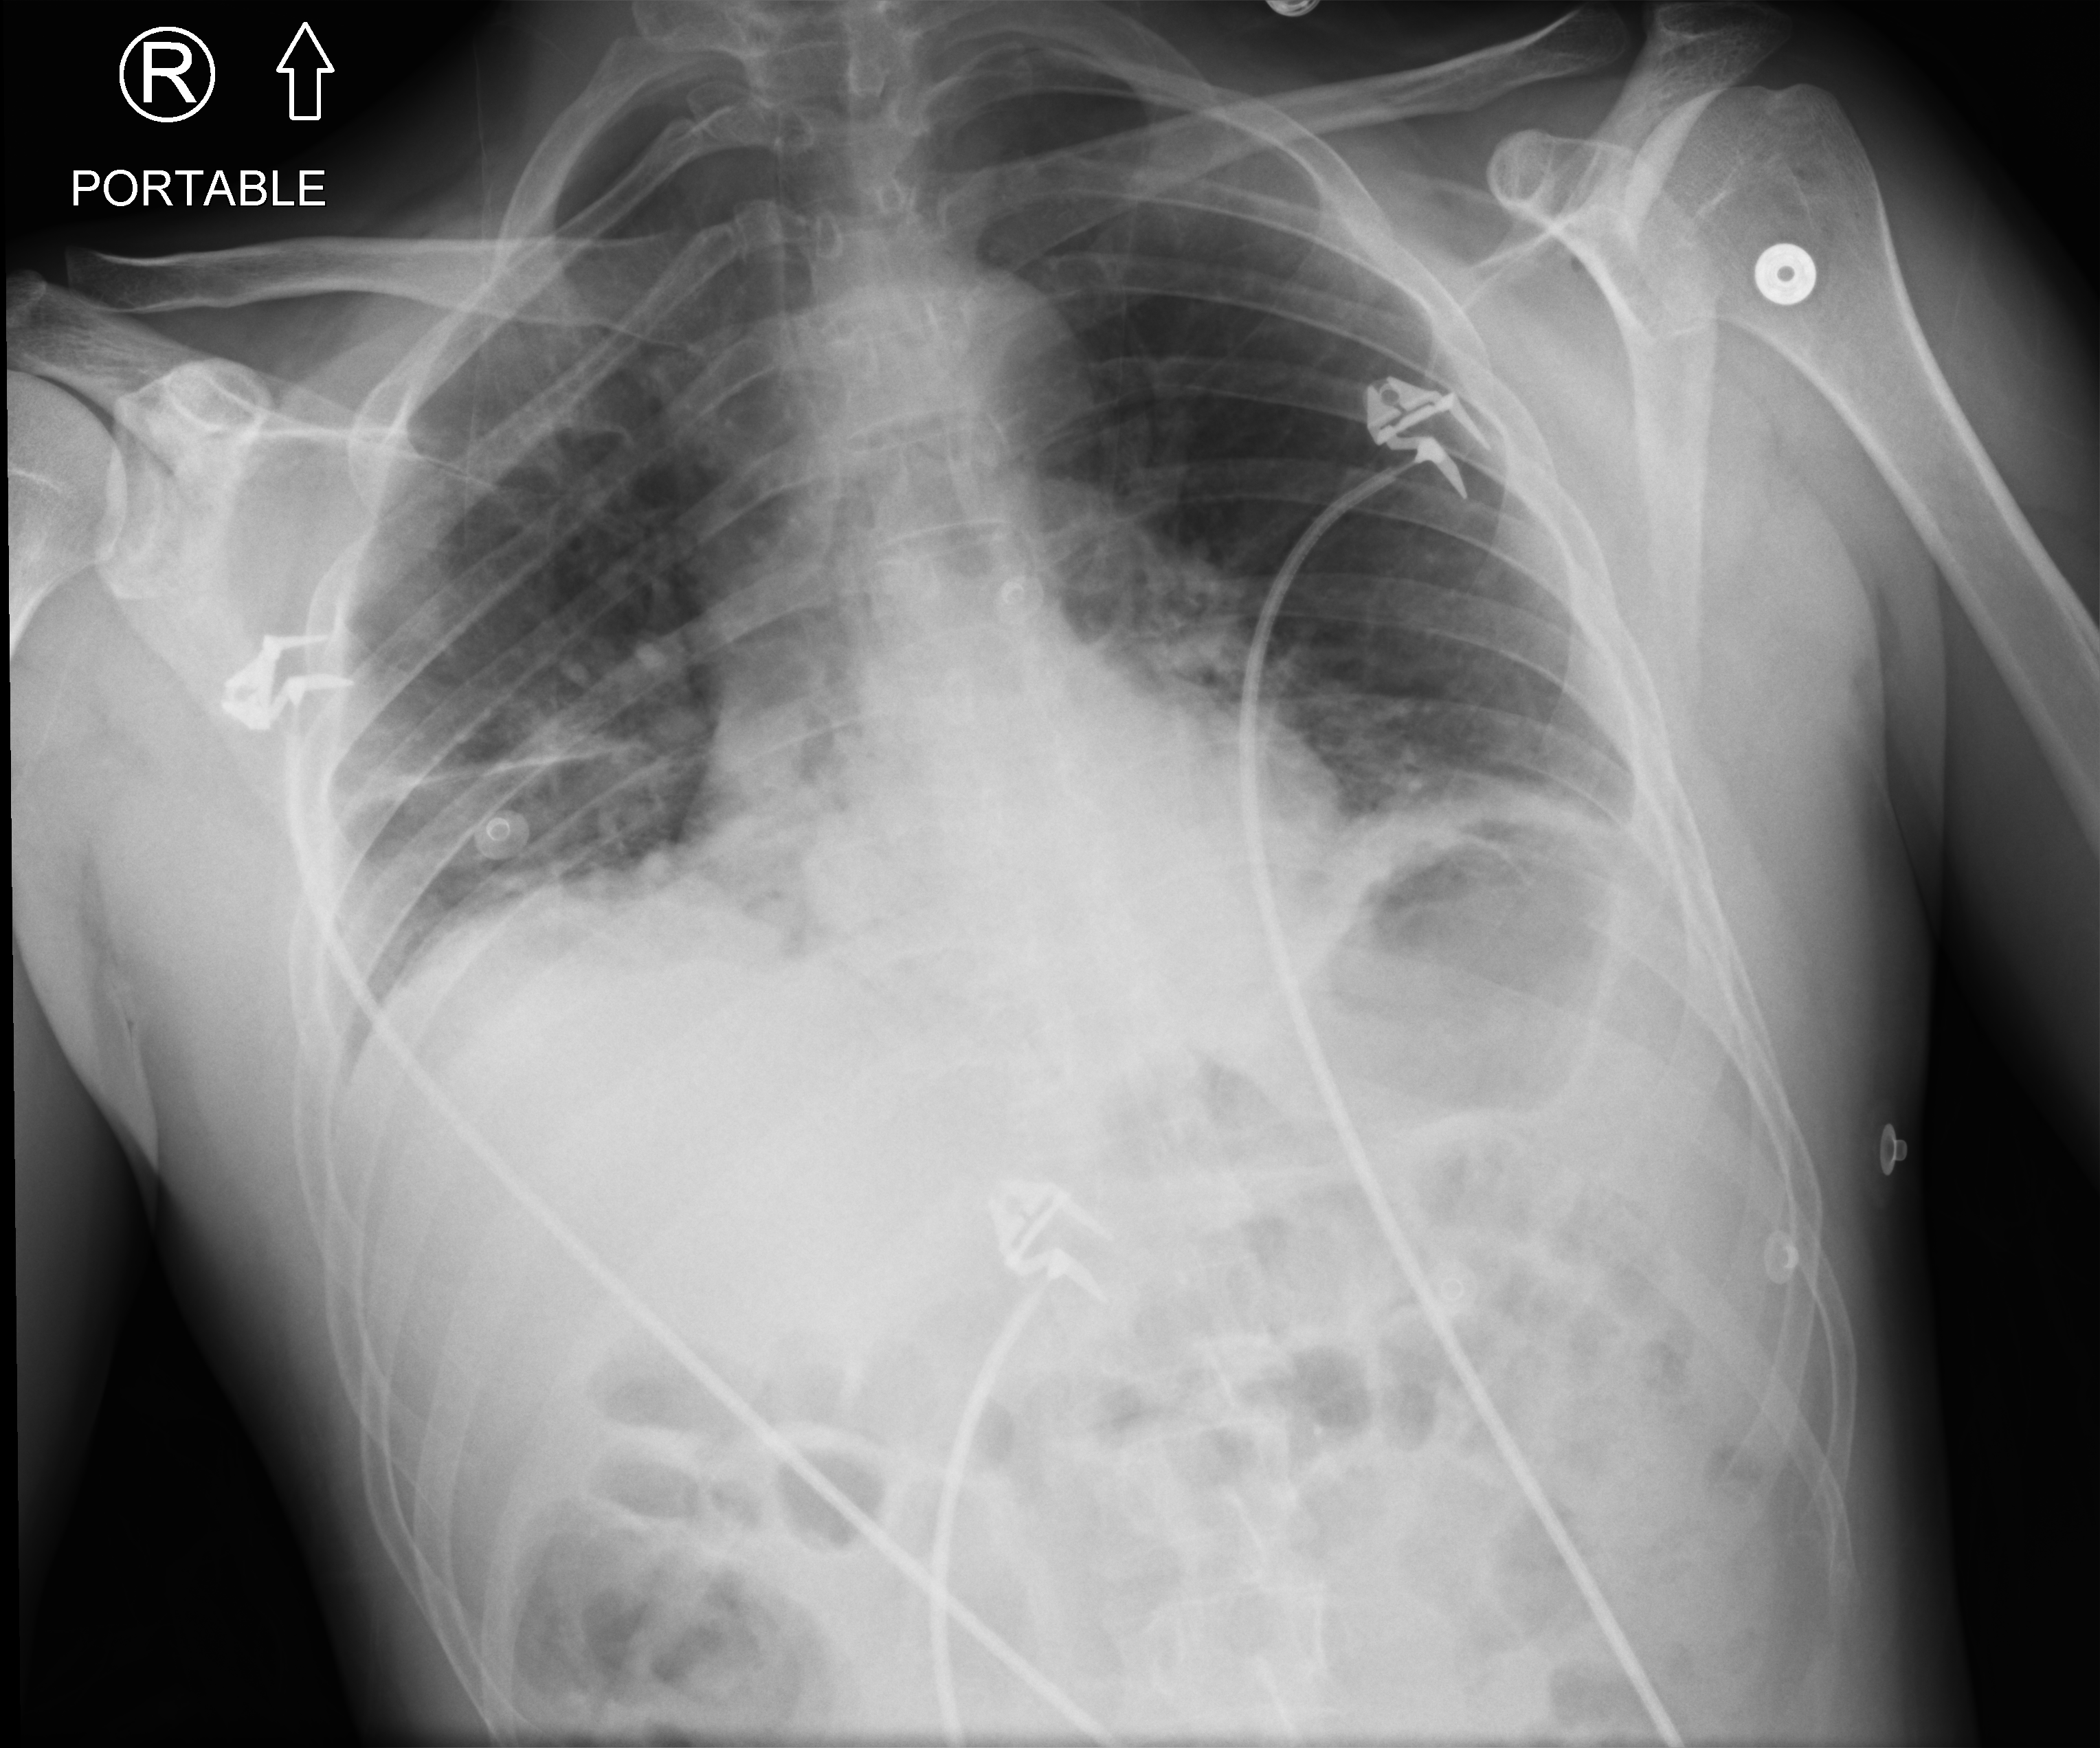
Chest X-ray (portable), anteroposterior (AP) projection. Male patient hospitalised with COVID-19, age 18–59 years.
From the hospital-stay record, not from the radiograph (when in the stay this image was taken is not recorded): admitted to intensive care during this hospital stay: no.